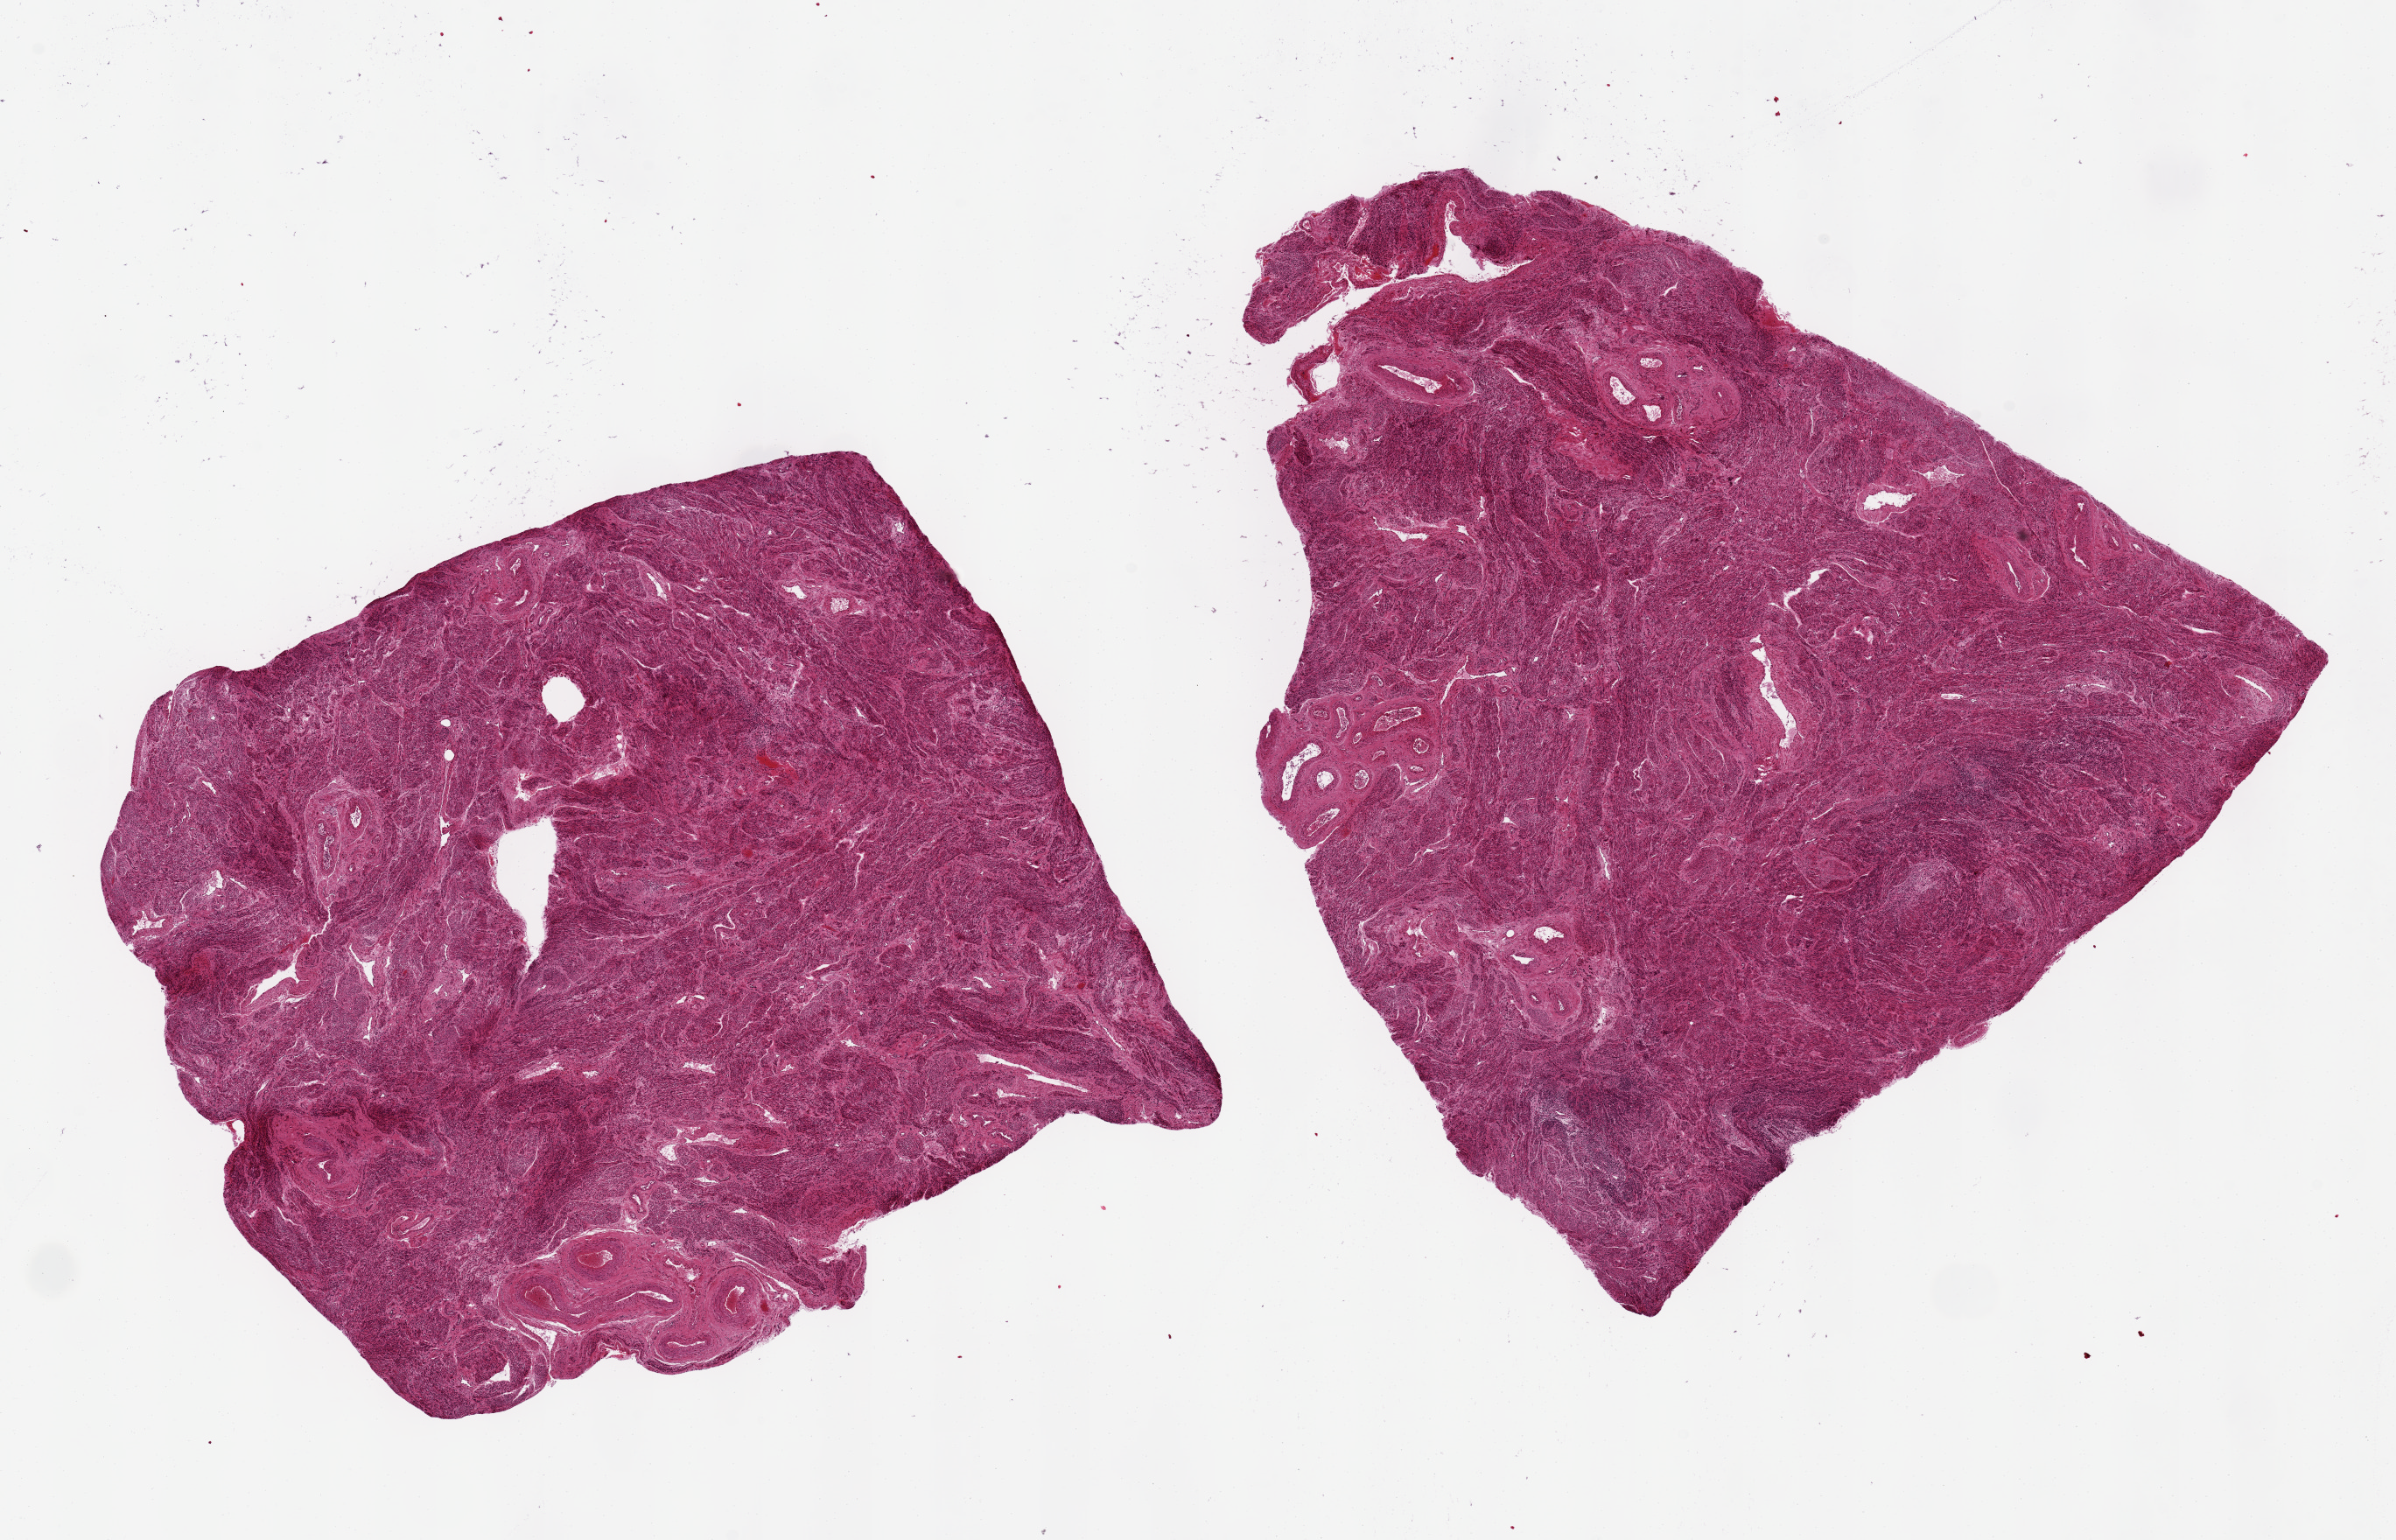
Whole-slide image, H&E stain, brightfield, low-resolution overview of the scanned area, about 21.7 x 13.9 mm, PAXgene-fixed, paraffin-embedded tissue, section of uterus (target tissue), donor tissue sample.
Review note (as recorded): 2 pieces, 9x8 & 8x7 mm; no endometrium, only myometrium.